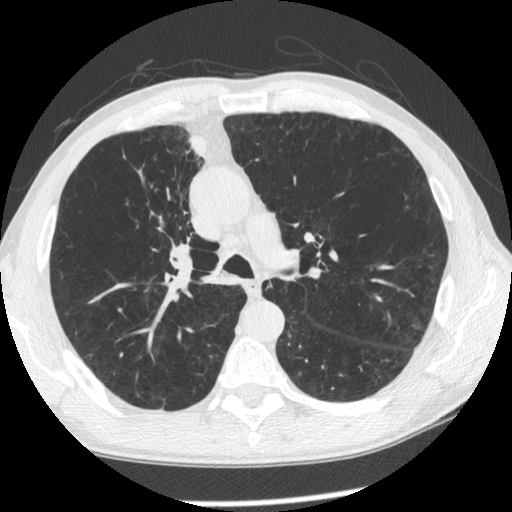
Low-dose screening chest CT, one axial slice. Slice 156 of 261 in the series (ordered by position). Reconstruction kernel STANDARD. Lung window (W 1500 / L -600 HU). 1.25 mm slice thickness. 512 × 512 image matrix.
Outlined on this slice (expert manual segmentation):
- lesion 1 (tumor, upper lobe of right lung): bounding box <188,134,205,156> (left, top, right, bottom; pixels)